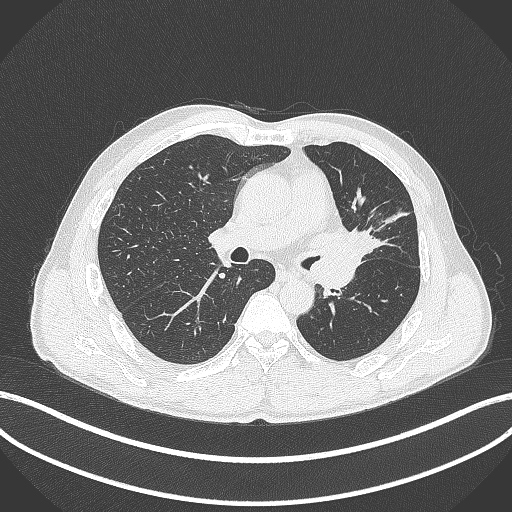
Chest CT, one axial slice. Position 243 of 429 along the scan axis. 120 kVp. Lung window (W 1500 / L -600 HU). 512 × 512 image matrix. Patient: male, 57 years. Case-level facts recorded for this patient, not image findings: clinical TNM (as recorded): T2b N0 M0.
Structures marked on this image (rectangle marked by the reading radiologist):
- lung tumour (recorded histology: squamous cell carcinoma): bounding box (x1, y1, x2, y2) in pixels: (319, 229, 379, 263)